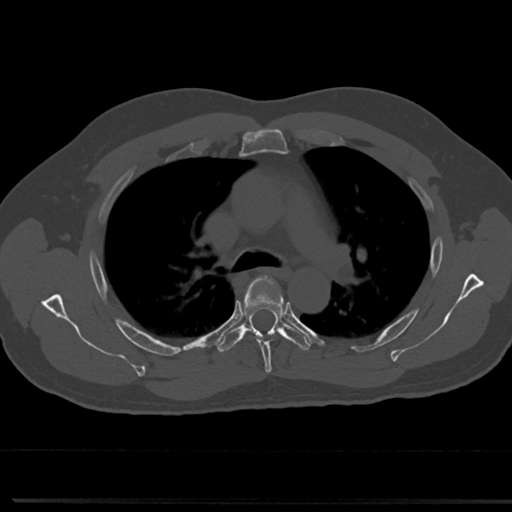
CT including the spine, one axial slice; slice 518 of 817 in the series (ordered by position); 120 kVp; bone window (W 1800 / L 400 HU); 0.5 mm slice thickness; 512 × 512 image matrix, field of view 355 × 355 mm. Male patient, age 61 years. From the clinical record (not read from this slice): primary cancer: prostate.
Outlined on this slice (semi-automatic segmentation, software-assisted and operator-edited):
- T4 vertebra: bounding box [x1, y1, x2, y2] px = [241, 275, 287, 363]
- T5 vertebra: [221, 306, 310, 349]